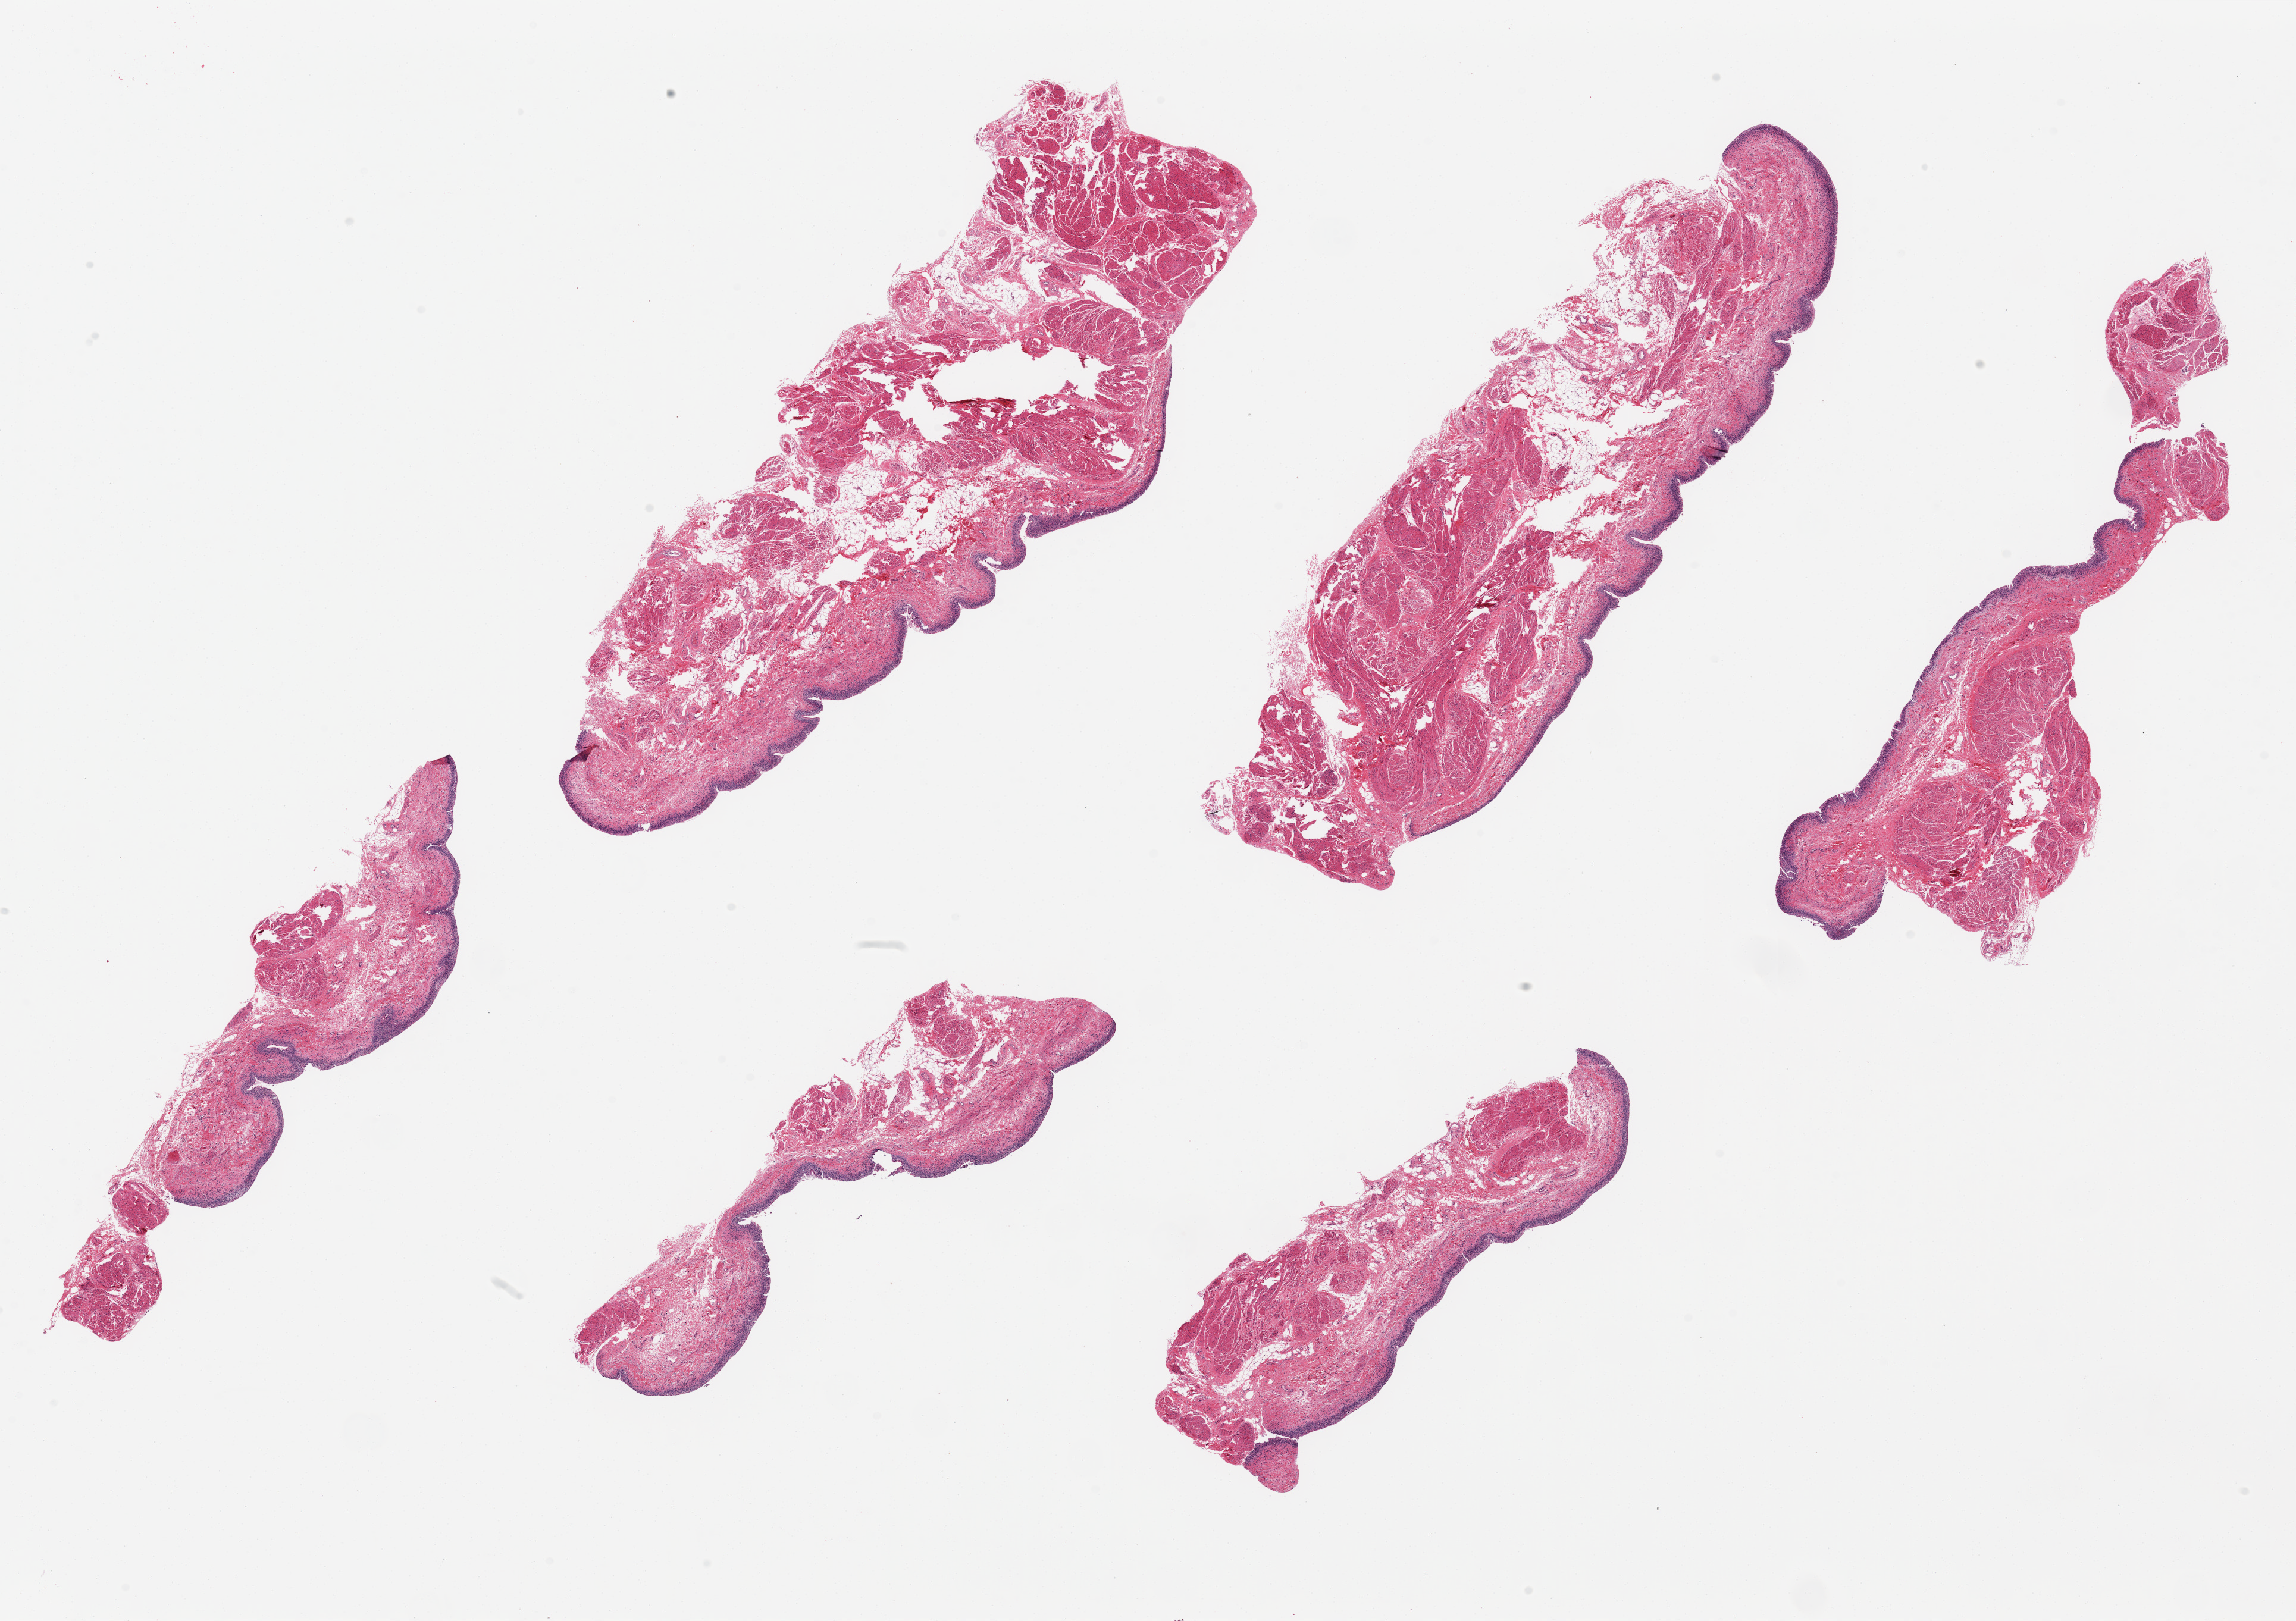
Digitized haematoxylin and eosin-stained section, low-resolution overview of the scanned area, about 30.5 x 21.5 mm. PAXgene-fixed paraffin-embedded (PFPE) section. Section of urinary bladder (target tissue). Donor tissue sample.
• review note (as recorded): 6 pieces, ~9x3mm. Urothelium unusally well-preserved, ~2-3% of thickness